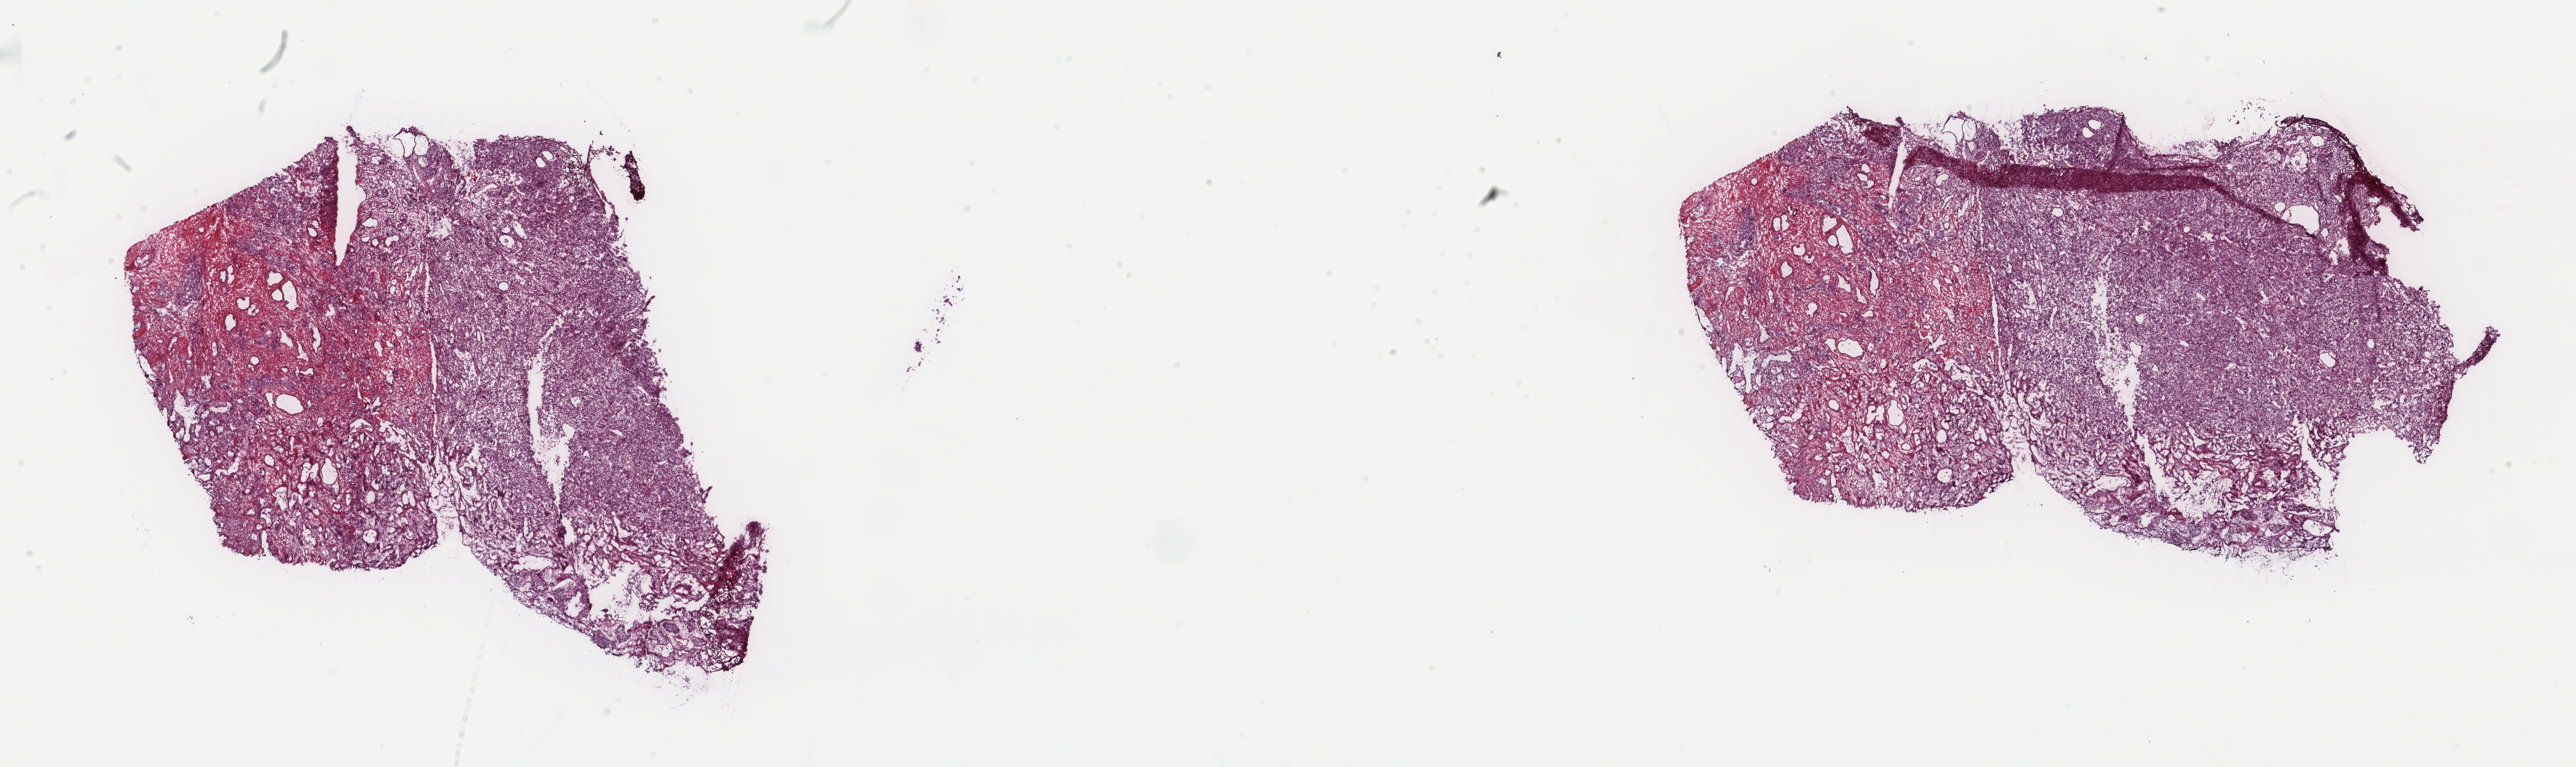
Hematoxylin and eosin (H&E) stained whole-slide image, whole scanned area (about 28.1 x 8.4 mm, acquisition: 40x scan) shown as a low-resolution overview. Frozen section from the top of the tissue portion. Uterus, primary tumour sample. Patient: female, age at initial diagnosis 84 years. Histologic grade: G3 (poorly differentiated). Composition of this section per pathologist review: tumour cells 60%, tumour nuclei 70%, normal cells 35%, stromal cells 4%, necrosis 1%. Inflammatory infiltration, as recorded: lymphocyte infiltration 5%, monocyte infiltration 0%, neutrophil infiltration 0%.
Histologic diagnosis: Serous cystadenocarcinoma, NOS (endometrium). Lymph nodes positive (case pathology): 0 of 11 examined. FIGO stage: IA.